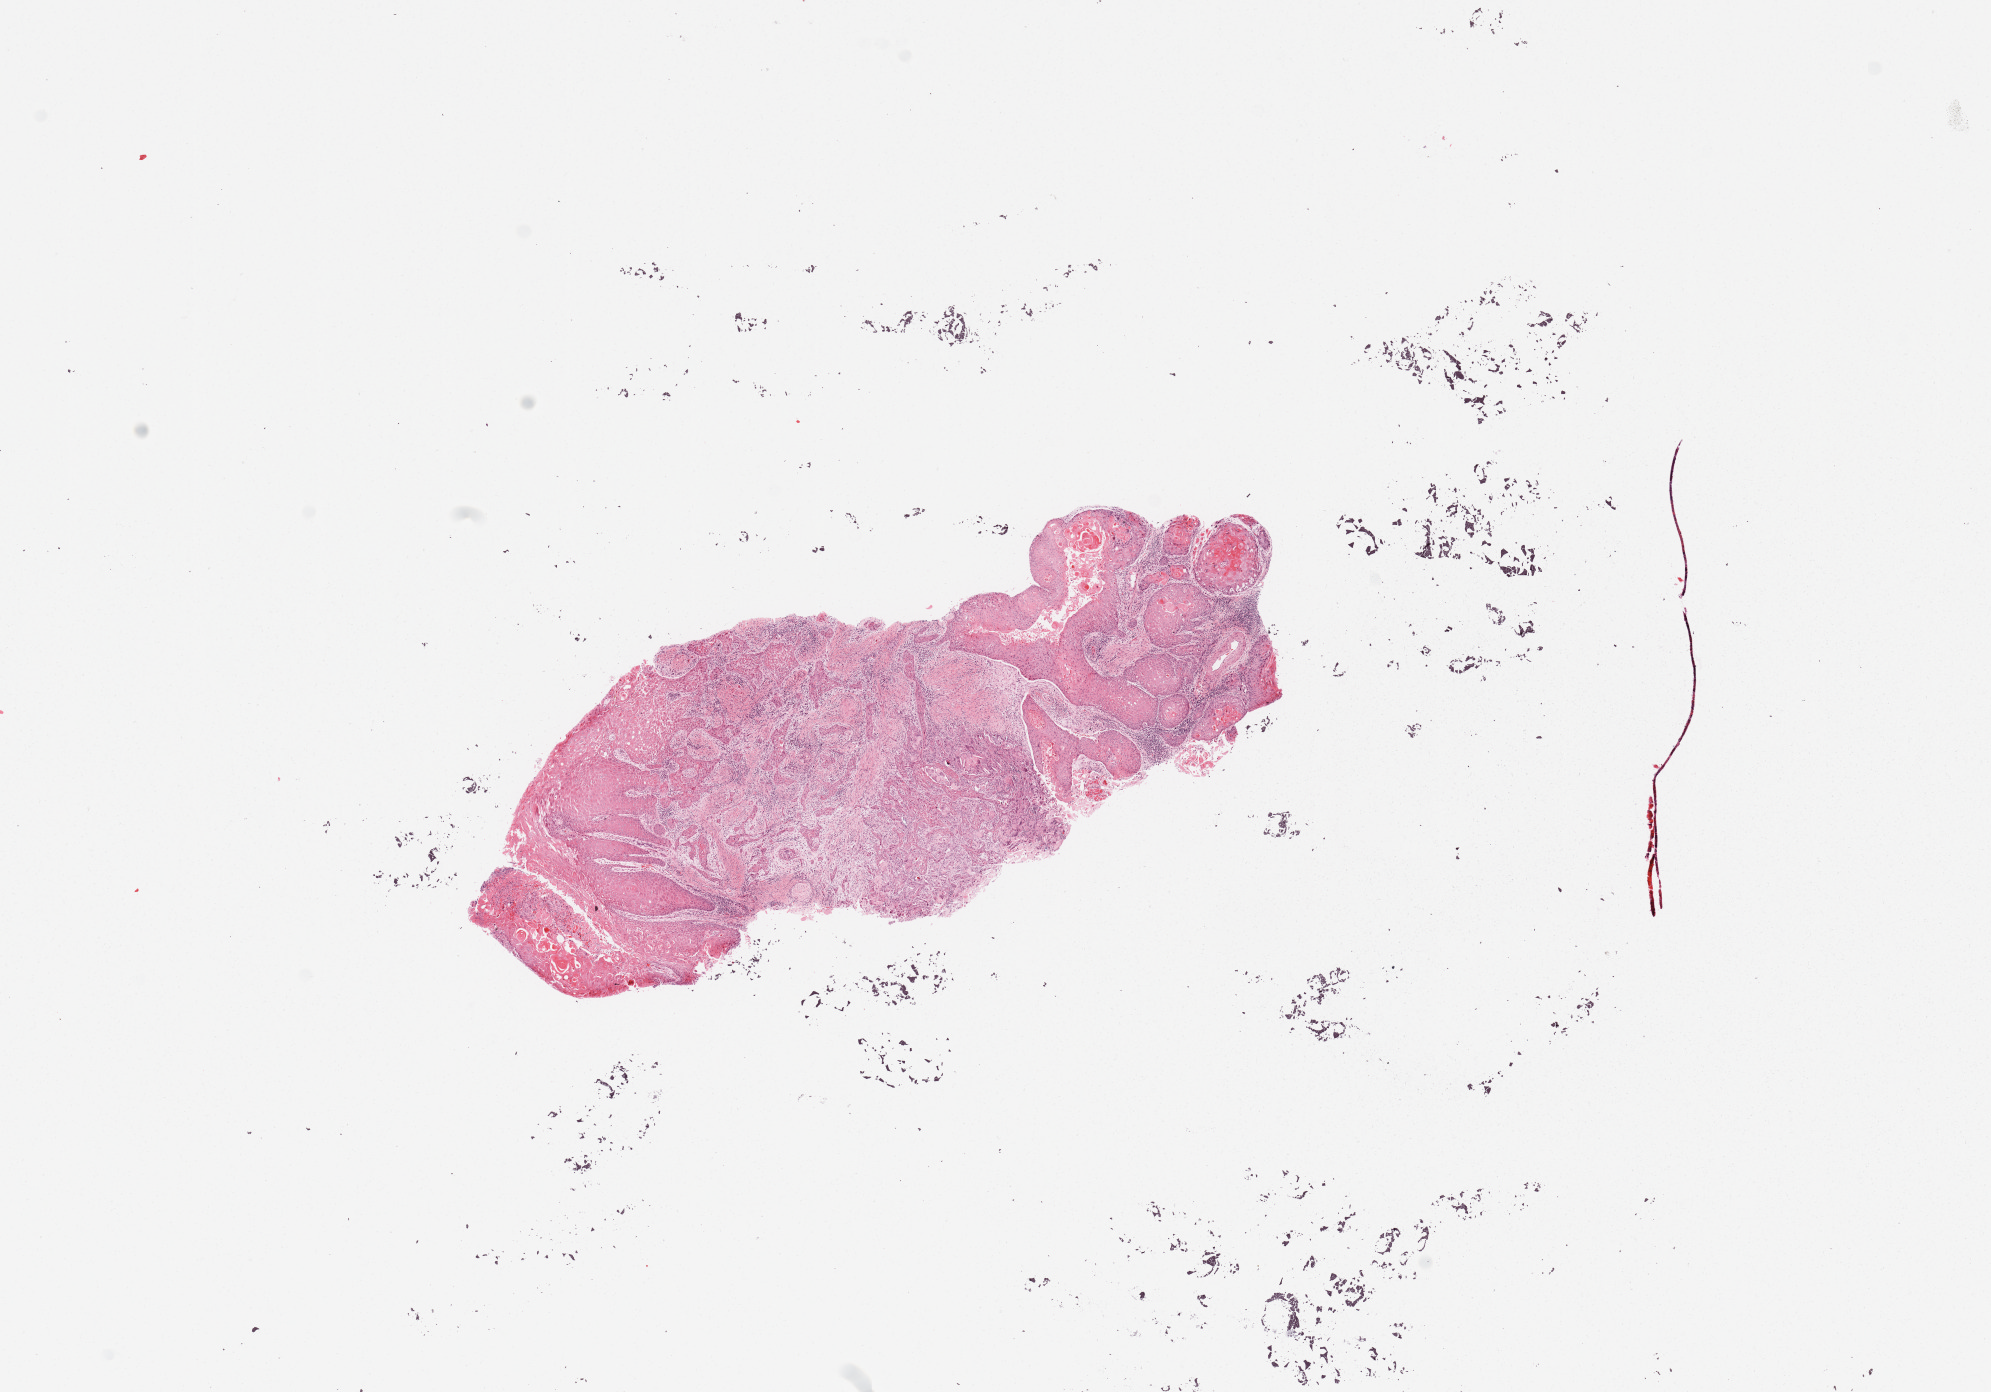
Digitized H&E-stained tissue section (whole slide) — low-resolution overview of the scanned area, about 15.8 x 11.0 mm; tumour tissue sample, sampled site: tongue. Male, 40 y/o. Histologic grade: G2 (moderately differentiated). Composition of this section per pathologist review: tumour nuclei 85%, necrosis 2%.
Histologic diagnosis: Squamous cell carcinoma, NOS (tongue, NOS). AJCC pathologic stage: III.